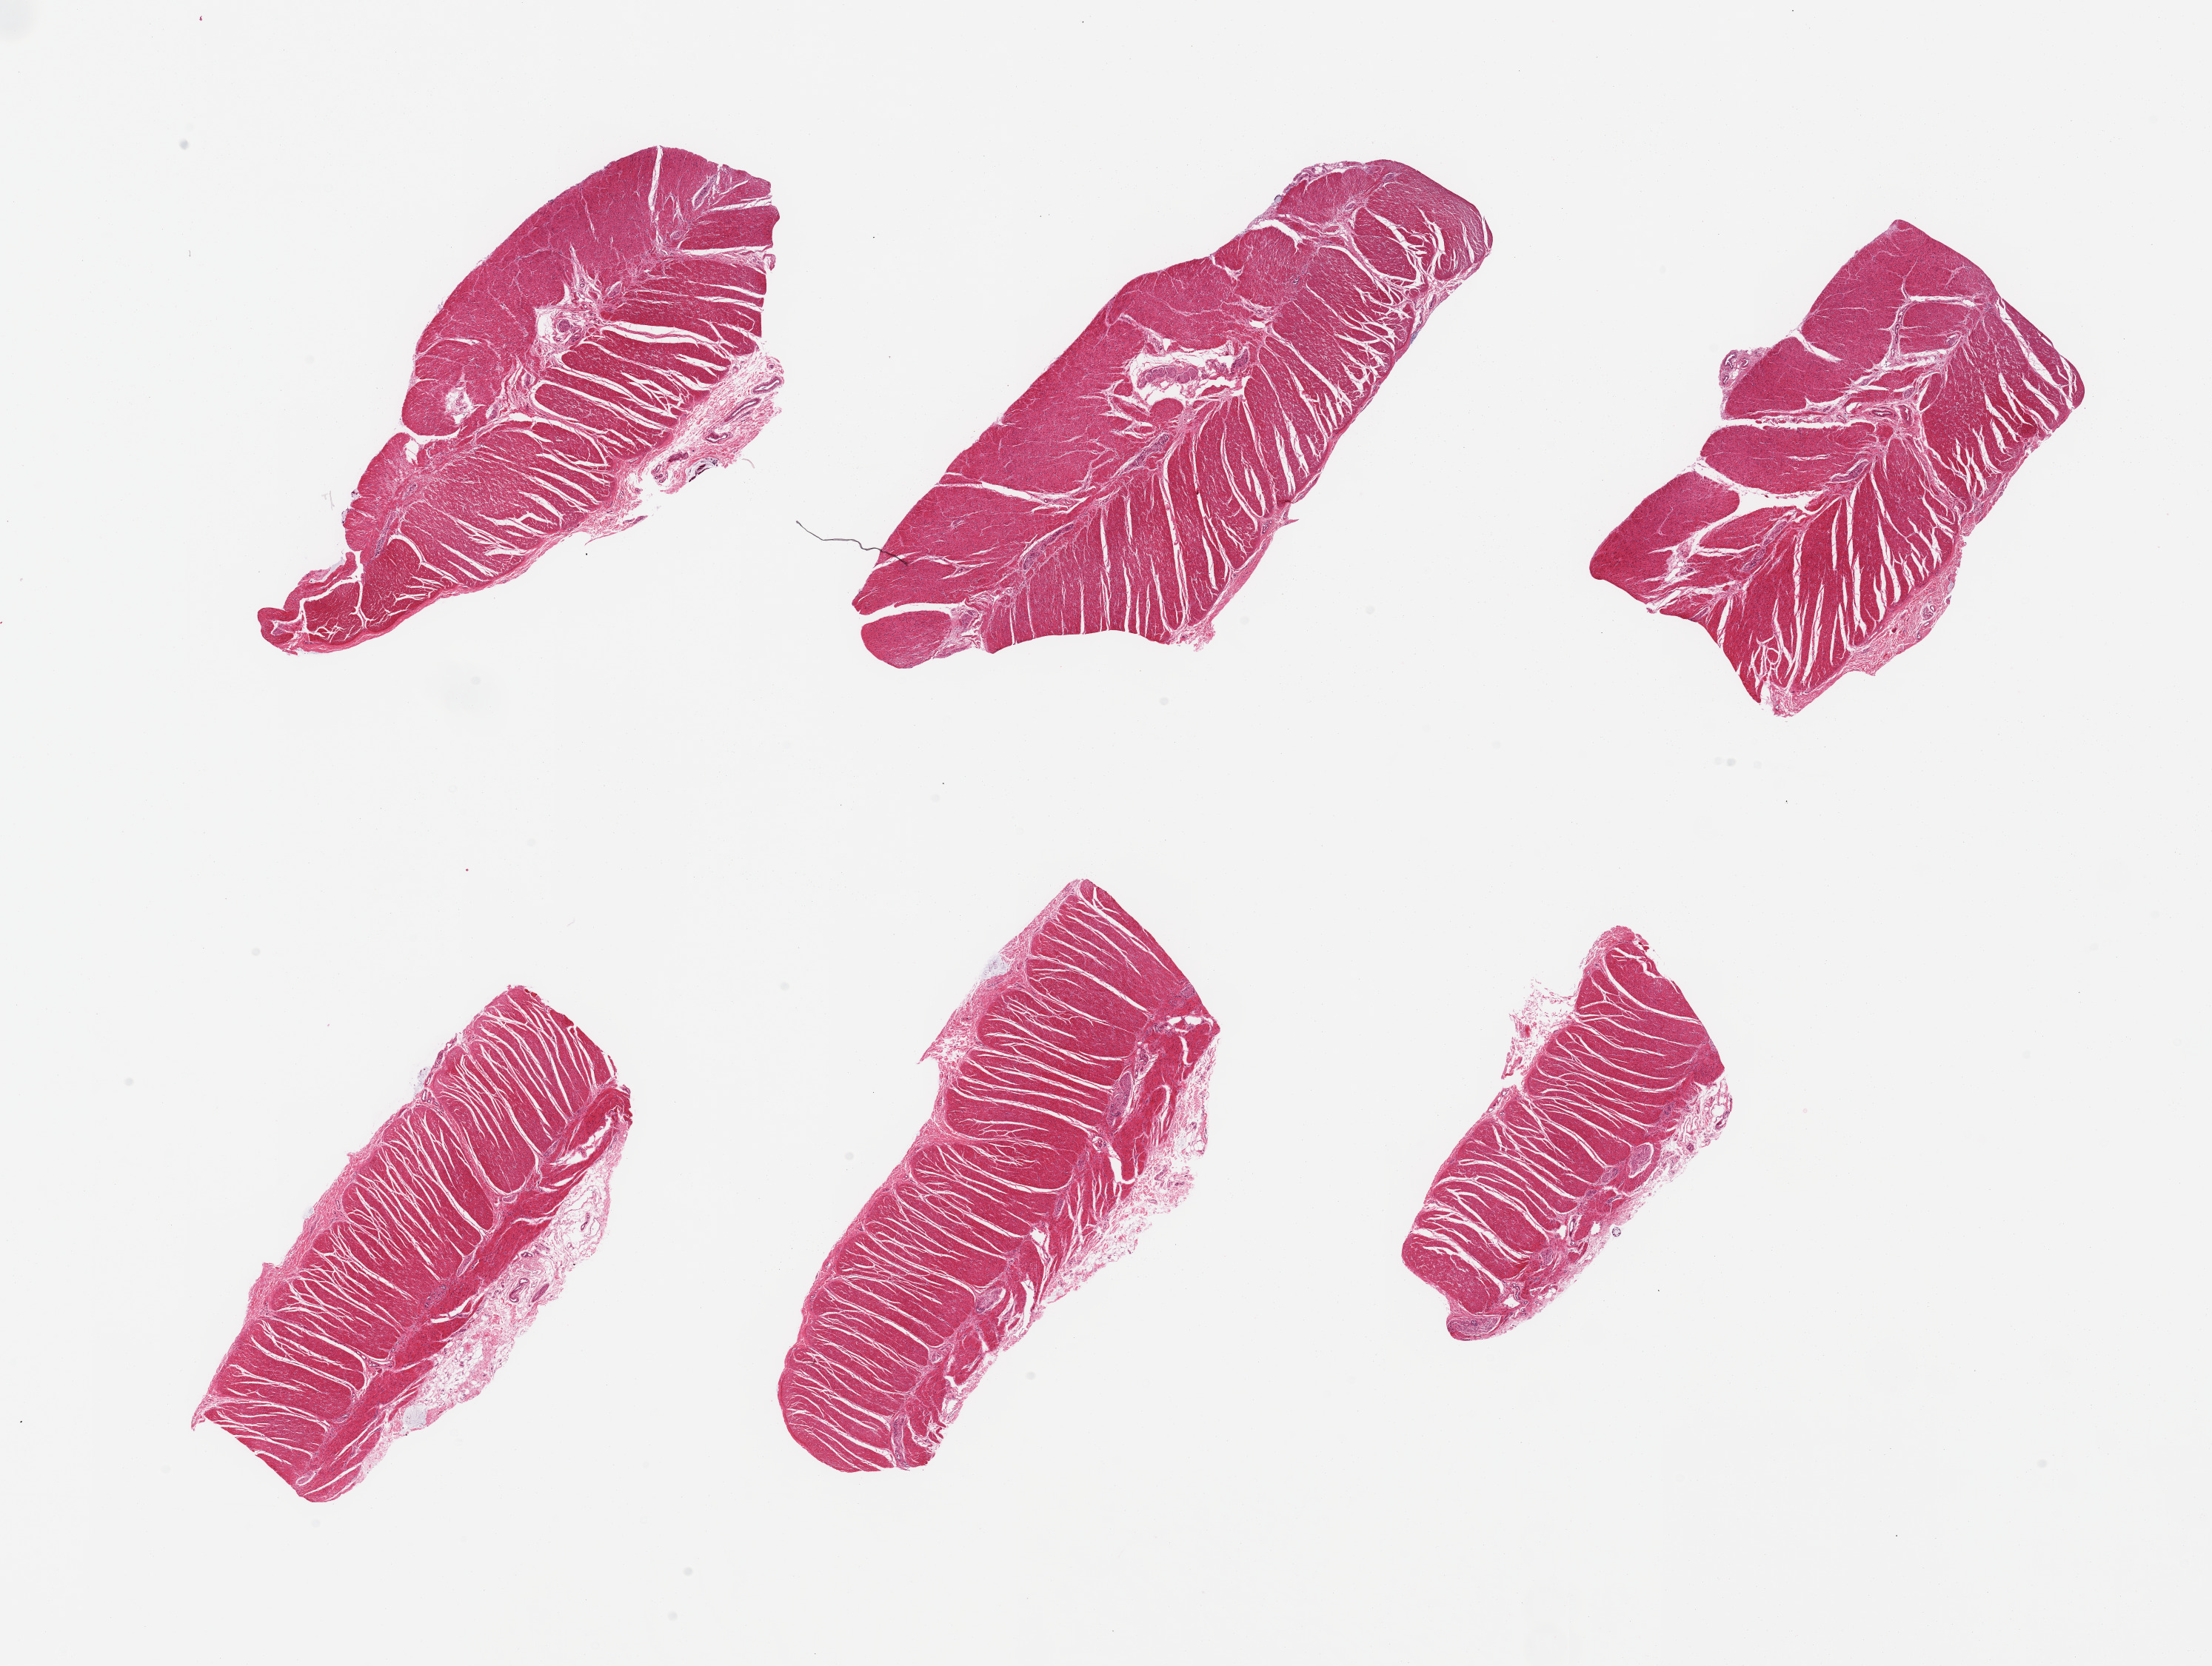
H&E whole-slide image, shown as a low-resolution overview of the whole scanned area (about 23.6 x 17.8 mm). PAXgene-fixed paraffin-embedded (PFPE) section. Section of sigmoid colon (target tissue). Tissue donor sample. Donor sex: male.
Reviewer comment on this tissue sample: 6 pieces, confirmed target muscularis.